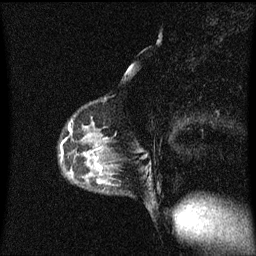
Breast MRI (dynamic contrast-enhanced), one sagittal slice; position 34 of 60 along the scan axis; dynamic contrast-enhanced series, image 2 of 3 at this slice position (ordered by acquisition); 1.5 T; TE 4.2 ms, TR 8.4 ms; 2 mm slice thickness; 256 × 256 image matrix, field of view 200 × 200 mm. Patient: female, 40 years.
Structures marked on this image (semi-automatic segmentation, software-assisted and operator-edited):
- analysis volume of interest (the breast-tissue region the enhancement analysis was run in; not a lesion): bounding box (x1, y1, x2, y2) in pixels: (83, 172, 118, 193)
- tumour enhancement mask (voxels above the 70 % enhancement threshold inside the analysis volume of interest): (98, 180, 101, 183)